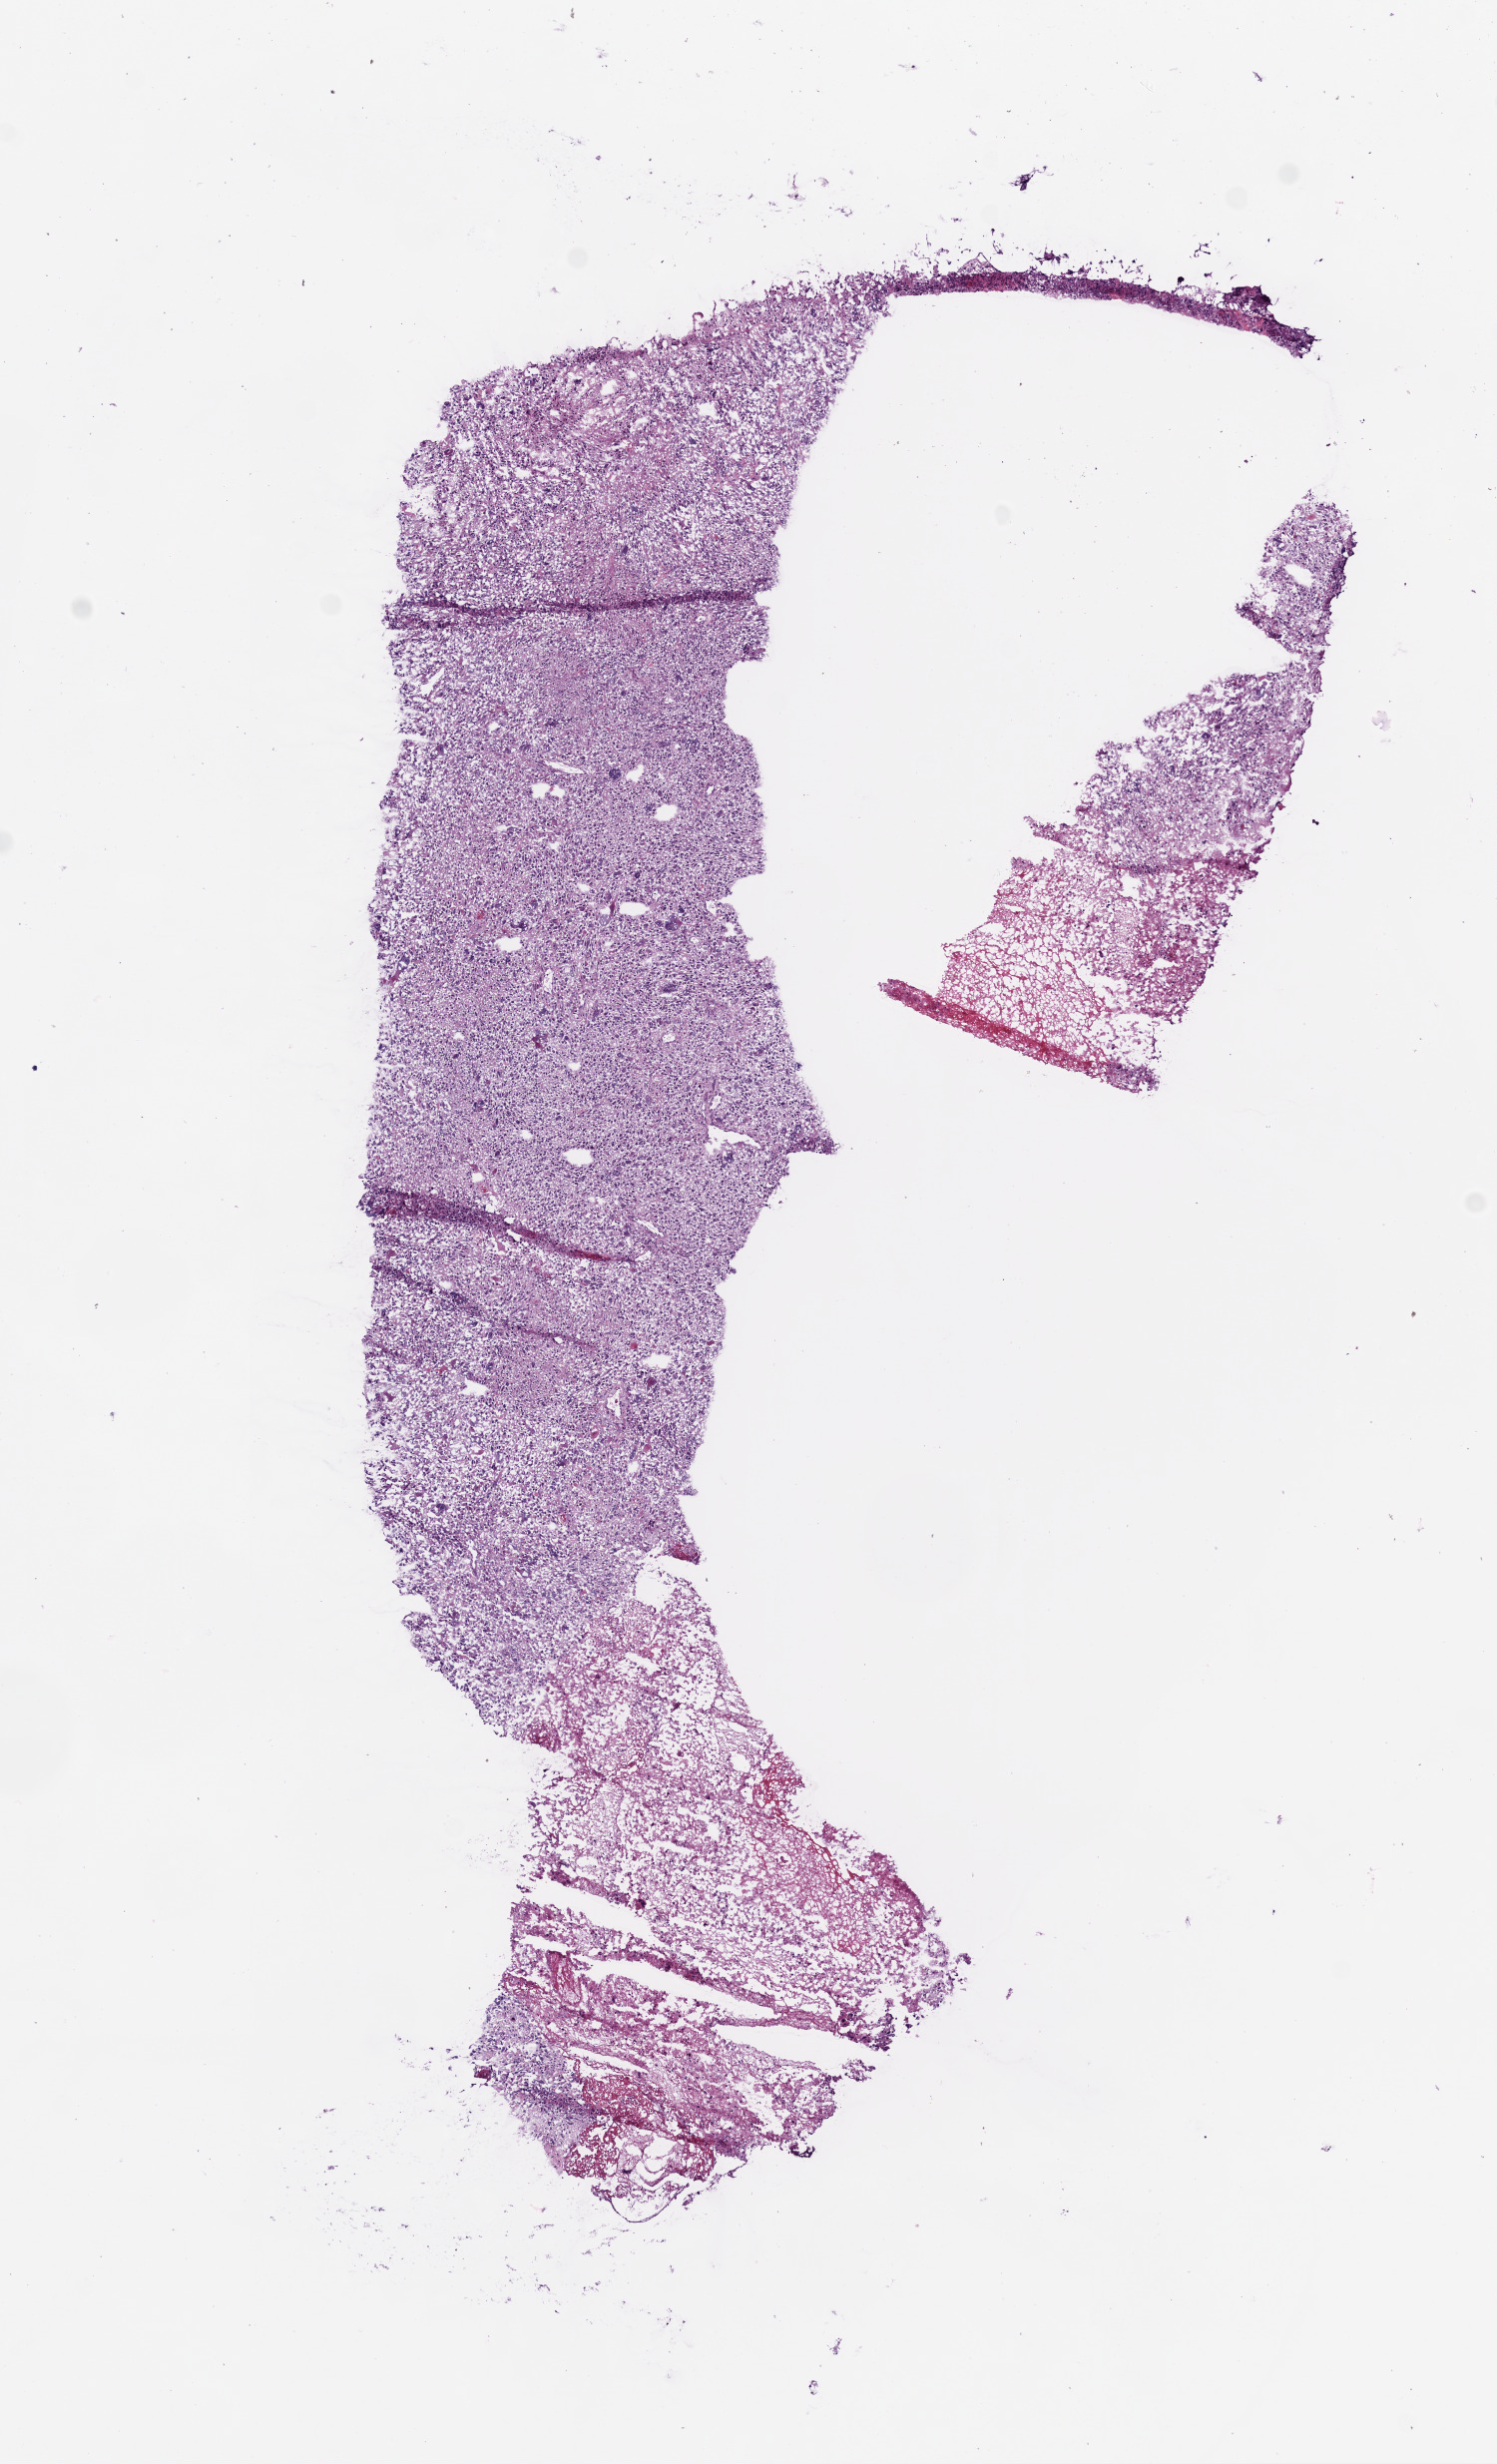
Whole-slide histology image, Hematoxylin and eosin (H&E) stained, low-resolution overview of the scanned area, about 6.0 x 9.9 mm (acquisition: 20x scan), frozen section from the bottom of the tissue portion, brain, primary tumour sample. Patient: female, age at initial diagnosis 77 years. Composition of this section per pathologist review: tumour cells 95%, tumour nuclei 80%.
Histologic diagnosis: Glioblastoma.